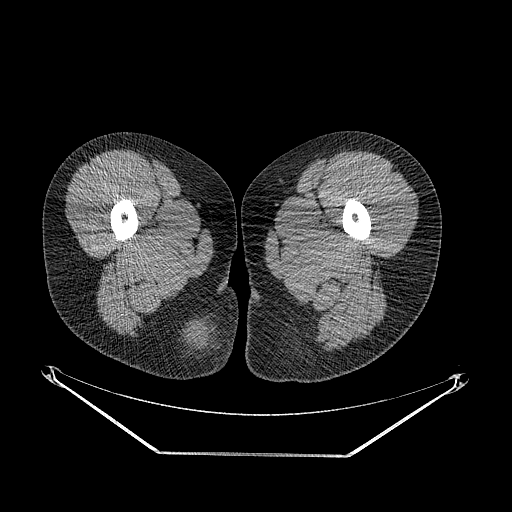
CT of an extremity soft-tissue mass (from a PET/CT study), one axial slice; slice 18 of 267 in the series (ordered by position); reconstruction kernel STANDARD; soft-tissue window (W 400 / L 40 HU); 3.75 mm slice thickness; 512 × 512 image matrix, field of view 500 × 500 mm. Female patient. Case-level facts recorded for this patient, not image findings: histological type: epithelioid sarcoma; grade: intermediate; site of the primary tumour: right buttock.
Annotated regions visible in this slice (expert contour drawn on MRI and transferred to this co-registered scan by the dataset authors):
- gross tumour volume including surrounding oedema: bounding box <176,311,234,384> (left, top, right, bottom; pixels)
- gross tumour volume (mass): <185,322,218,350>